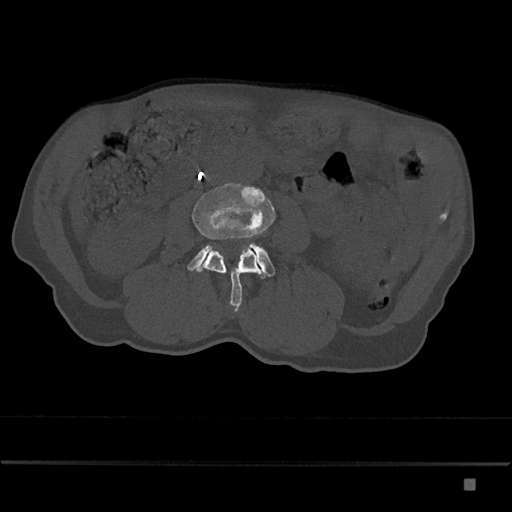
CT including the spine, one axial slice; slice 381 of 797 in the series (ordered by position); reconstruction kernel Br40s/3; 120 kVp; bone window (W 1800 / L 400 HU); 512 × 512 image matrix. Male patient, age 72 years. From the clinical record (not read from this slice): primary cancer: prostate.
Structures marked on this image (semi-automatic segmentation, software-assisted and operator-edited):
- L3 vertebra: bounding box [x1, y1, x2, y2] px = [192, 182, 275, 312]
- L4 vertebra: [187, 243, 275, 279]